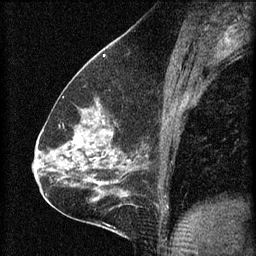
Breast MRI (dynamic contrast-enhanced), one sagittal slice. Position 35 of 60 along the scan axis. 3 images stored at this slice position (order not interpretable as contrast timing). 1.5 T. TE 4.2 ms, TR 8.2 ms. 2 mm slice thickness. 256 × 256 image matrix, field of view 180 × 180 mm. Female patient, age 59 years.
Outlined on this slice (semi-automatic segmentation, software-assisted and operator-edited):
- analysis volume of interest (the breast-tissue region the enhancement analysis was run in; not a lesion): bounding box <61,104,134,161> (left, top, right, bottom; pixels)
- tumour enhancement mask (voxels above the 70 % enhancement threshold inside the analysis volume of interest): <61,104,105,159>